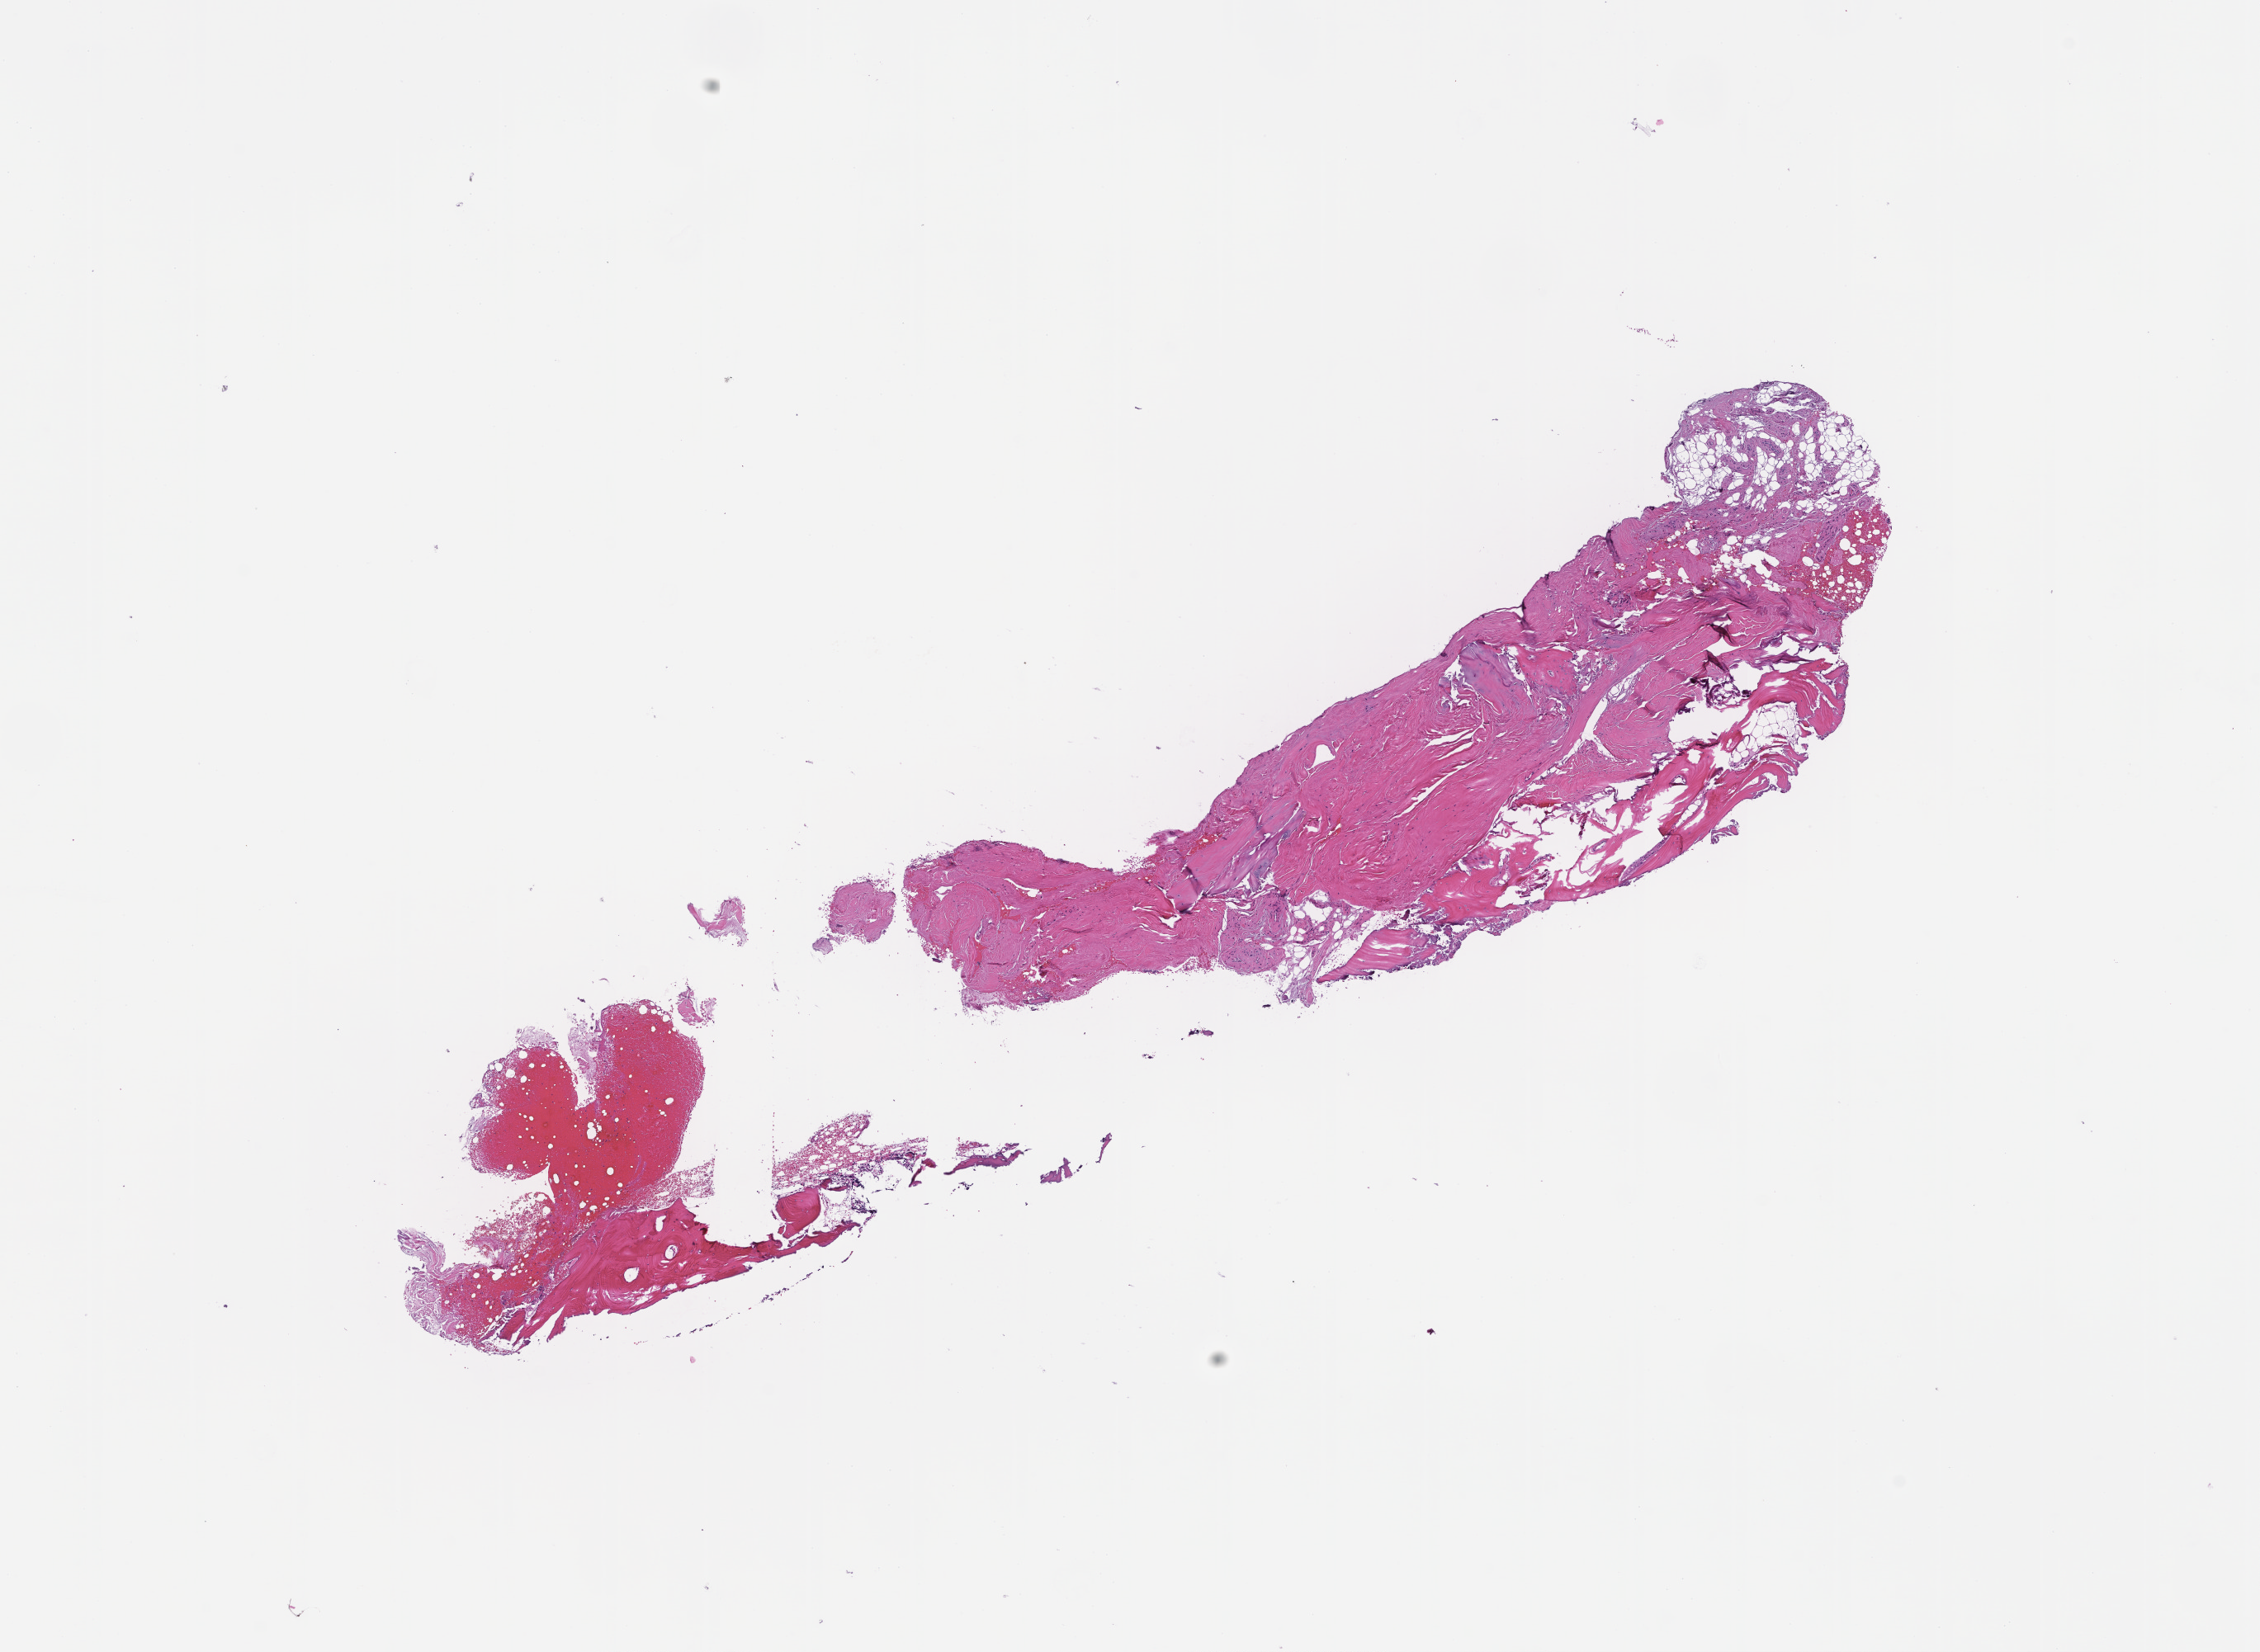
Whole-slide image, H&E stain — low-resolution overview of the scanned area, about 11.1 x 8.1 mm. FFPE section. Tissue site: bone marrow. Specimen time point: collected at disease progression. Patient sex: male.
• this section: primary tumor
• diagnosis: Plasma Cell Myeloma